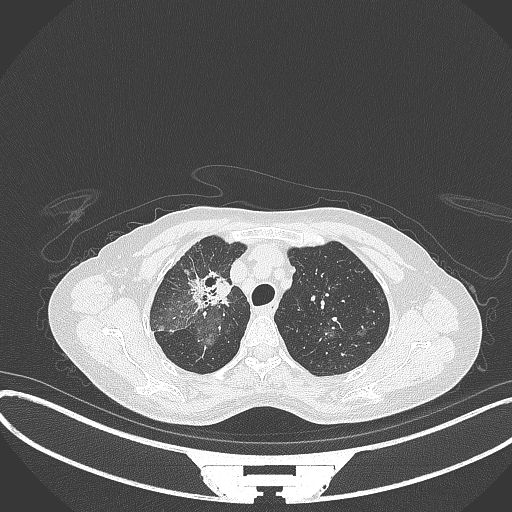
Chest CT, one axial slice. Slice 250 of 284 in the series (ordered by position). Reconstruction kernel B70f. Lung window (W 1500 / L -600 HU). 1 mm slice thickness. 512 × 512 image matrix, field of view 400 × 400 mm. Female patient, age 59 years. Case-level facts recorded for this patient, not image findings: clinical TNM (as recorded): T3 N0 M0.
Annotated regions visible in this slice (rectangle marked by the reading radiologist):
- lung tumour (recorded histology: adenocarcinoma): bounding box <186,271,237,310> (left, top, right, bottom; pixels)